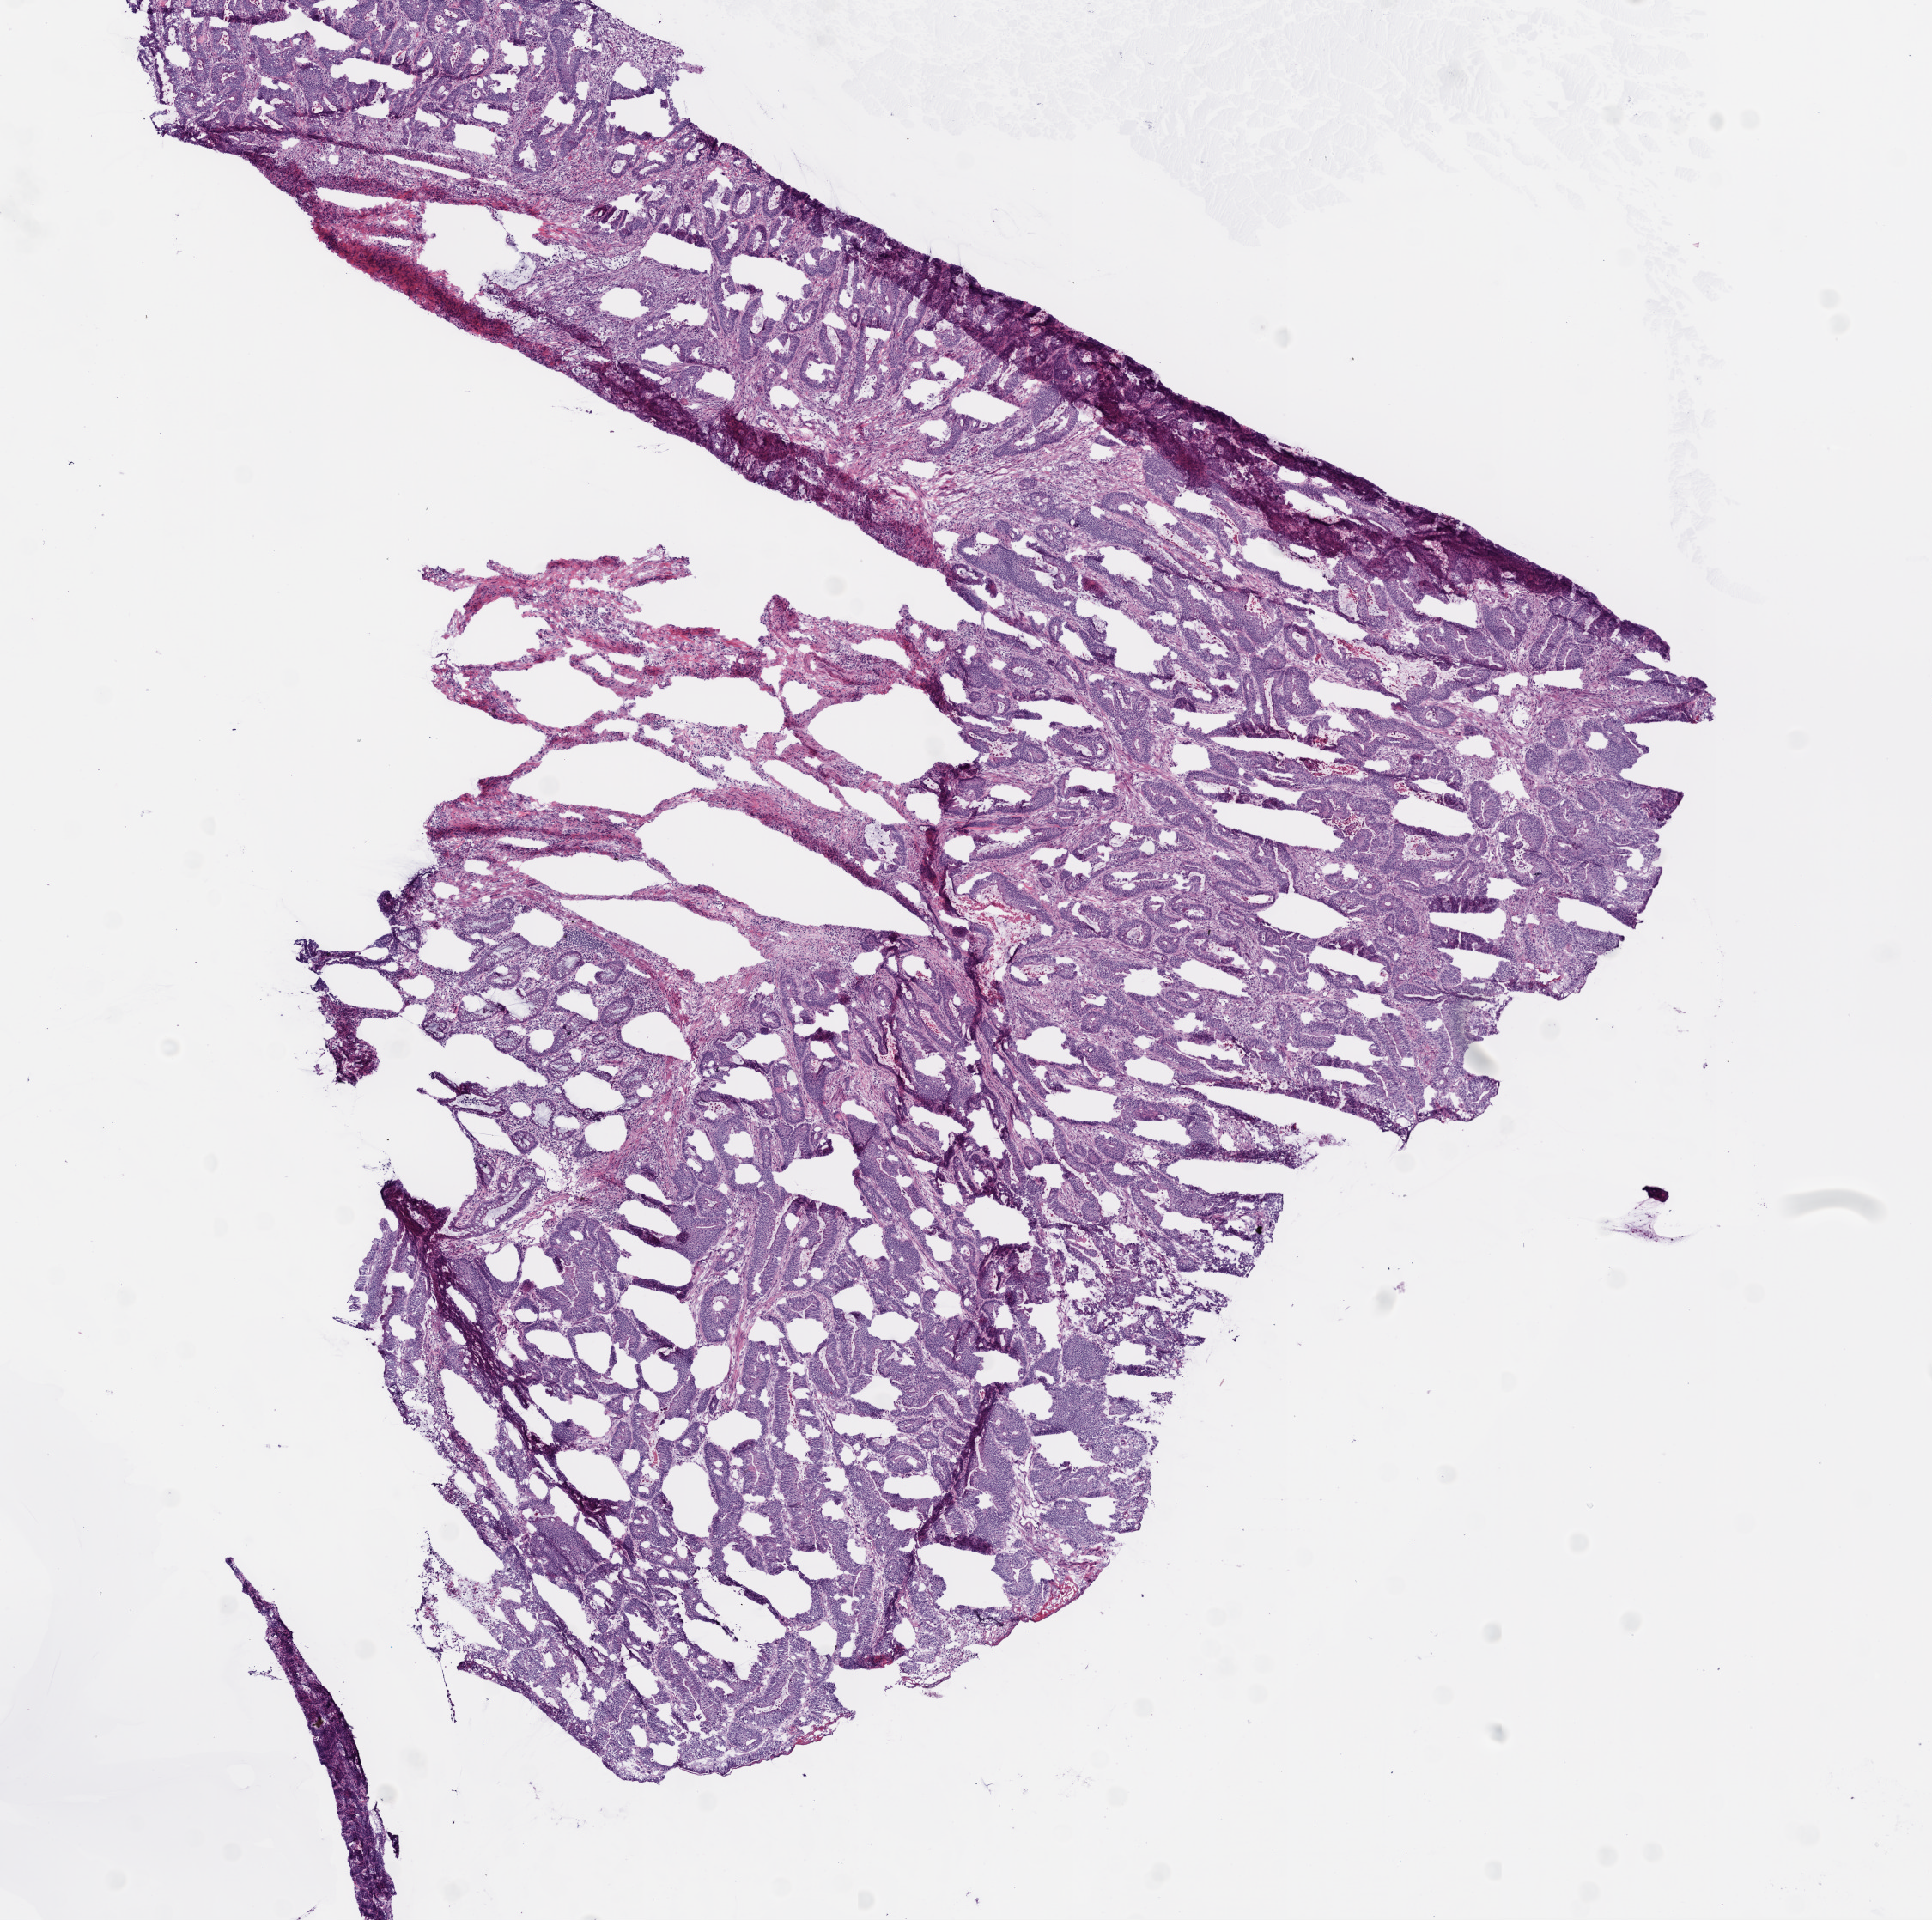
H&E whole-slide image — low-resolution overview of the scanned area, about 9.0 x 9.0 mm (acquisition: 20x scan). Frozen section from the bottom of the tissue portion. Sample: primary tumour, colon. Female patient. Slide review estimates, as recorded: tumour cells 85%, tumour nuclei 75%, normal cells 0%, stromal cells 10%, necrosis 5%.
Lymph nodes positive (case pathology): 0 of 21 examined. AJCC pathologic stage: II (5th edition). Diagnosis: Adenocarcinoma, NOS (ascending colon). TNM: T3 N0 M0.